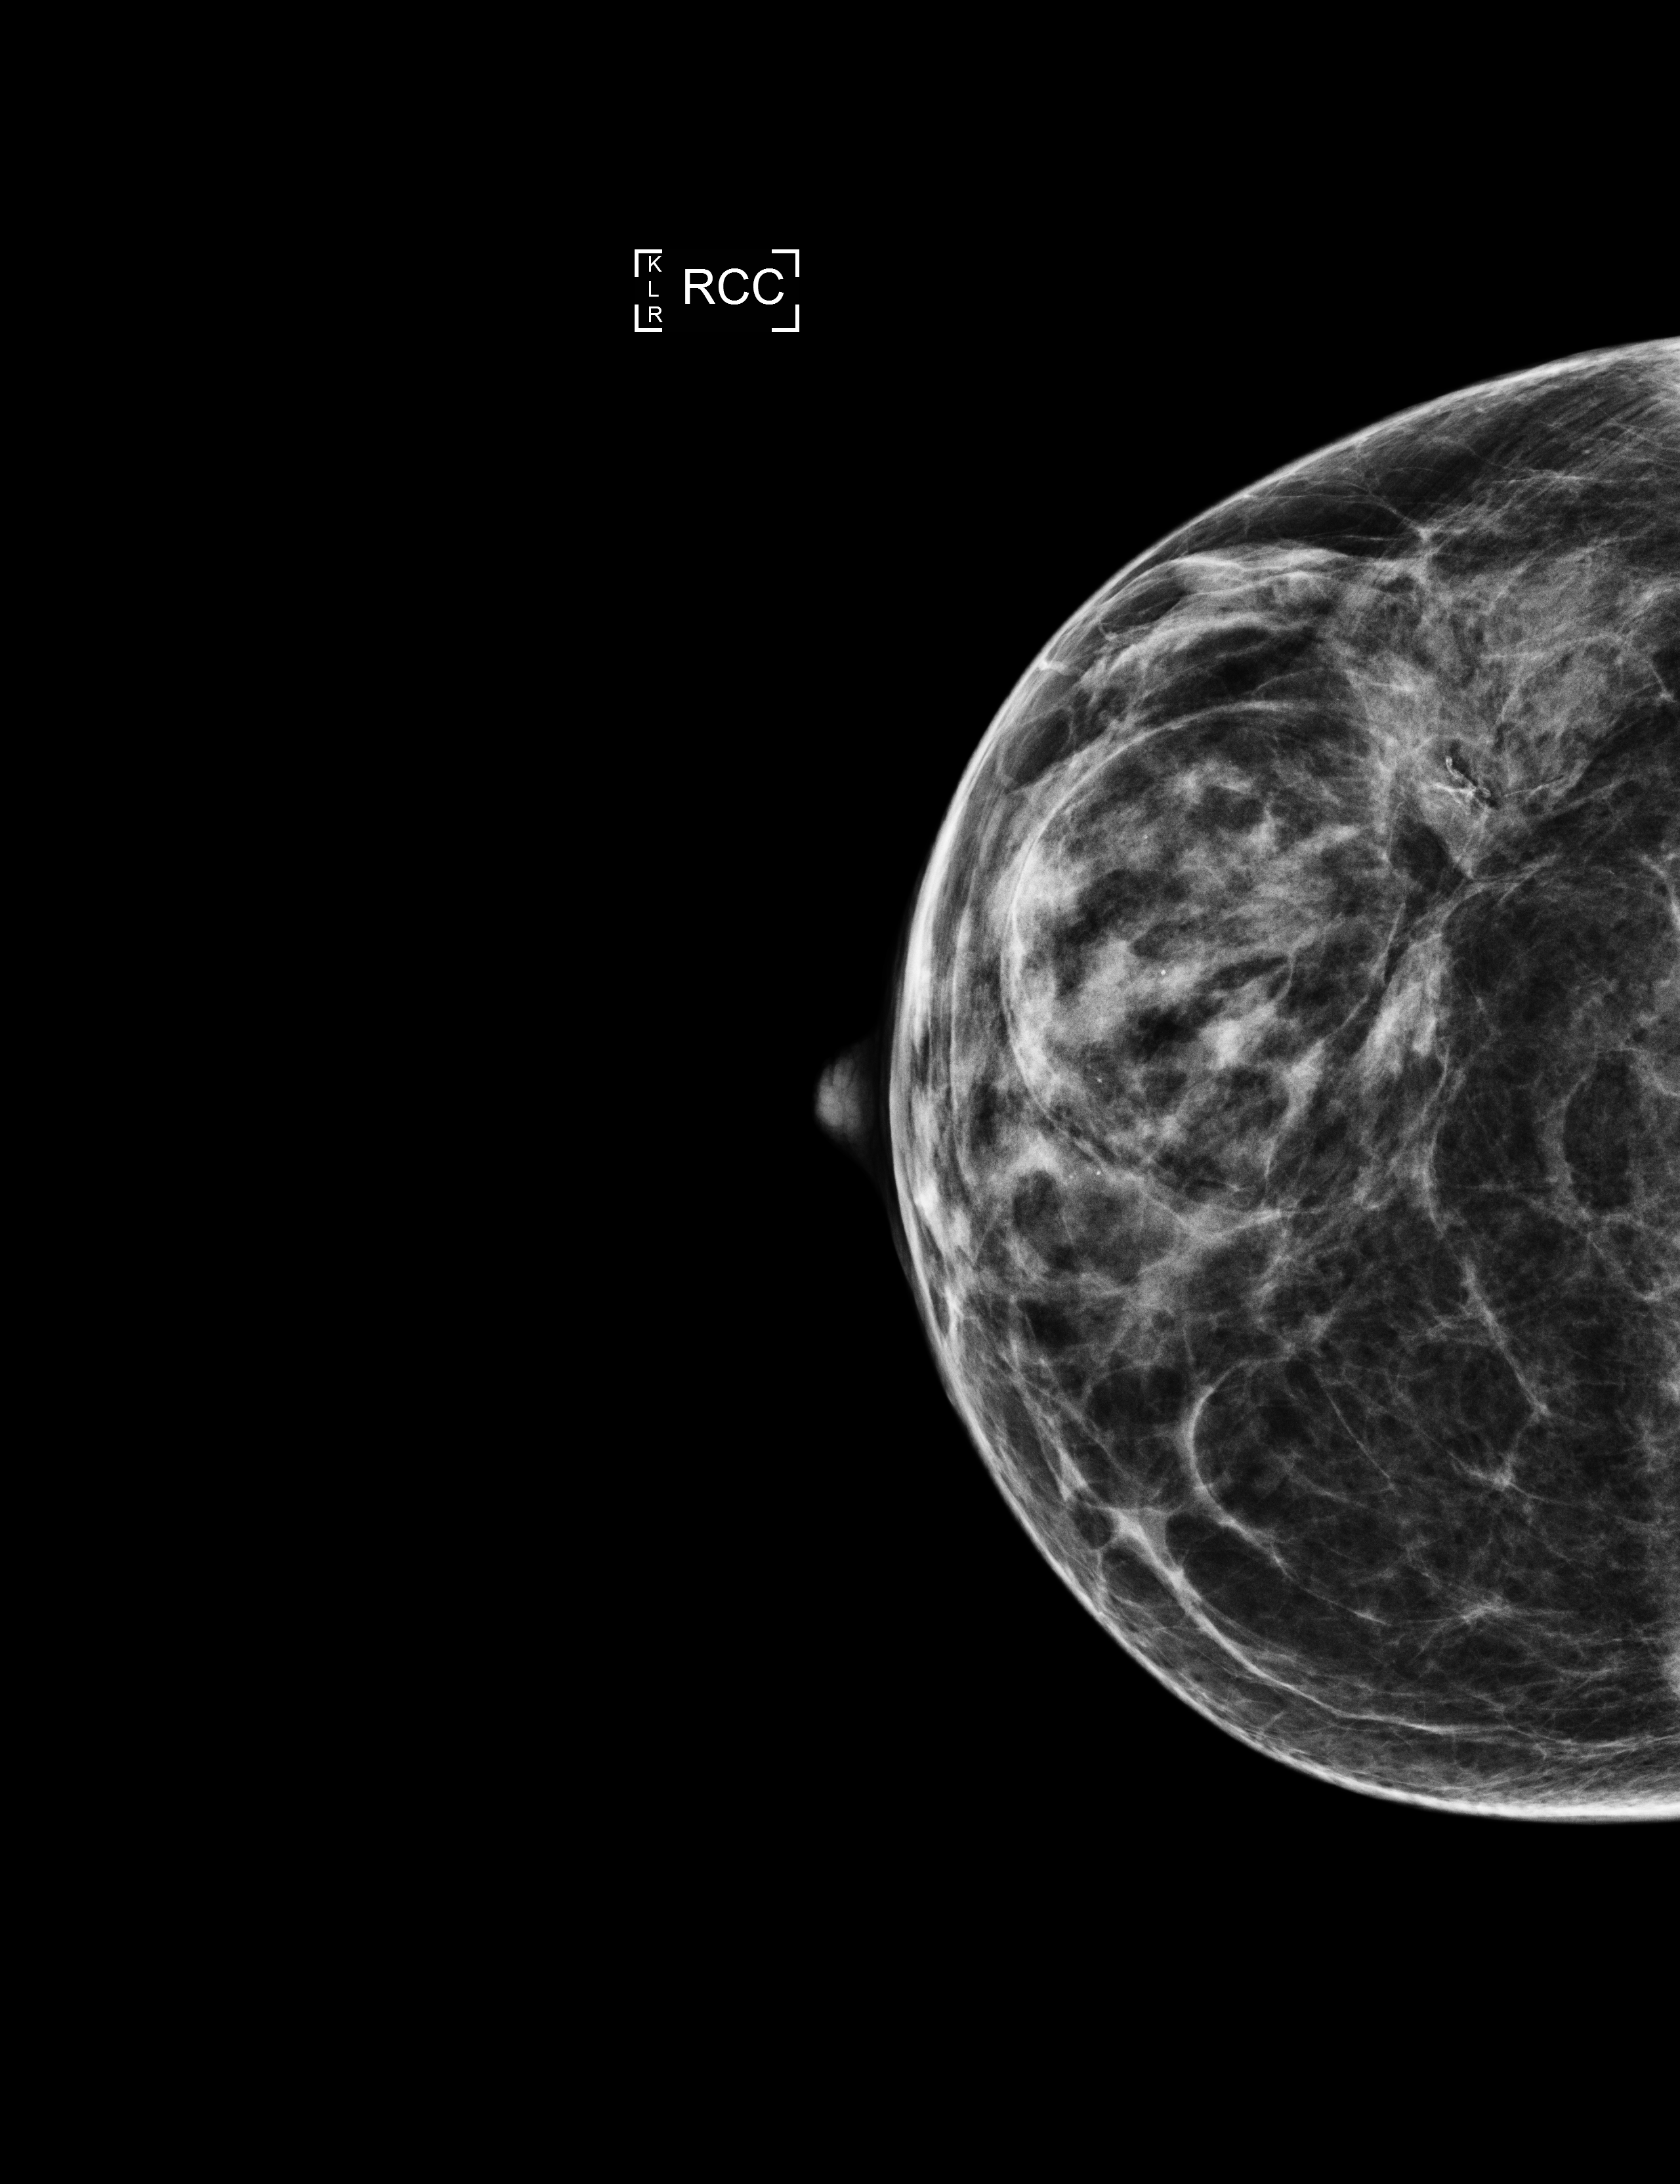
Digital mammogram (FFDM); right breast; craniocaudal (CC) view; annual screening mammography examination. Patient: female, 62 years.
BI-RADS breast density category at the screening exam (both breasts, scale 1–4): 3. Final BI-RADS category for the screening round (tomosynthesis exam, both breasts): category 2. Recall: no recall after this screen.